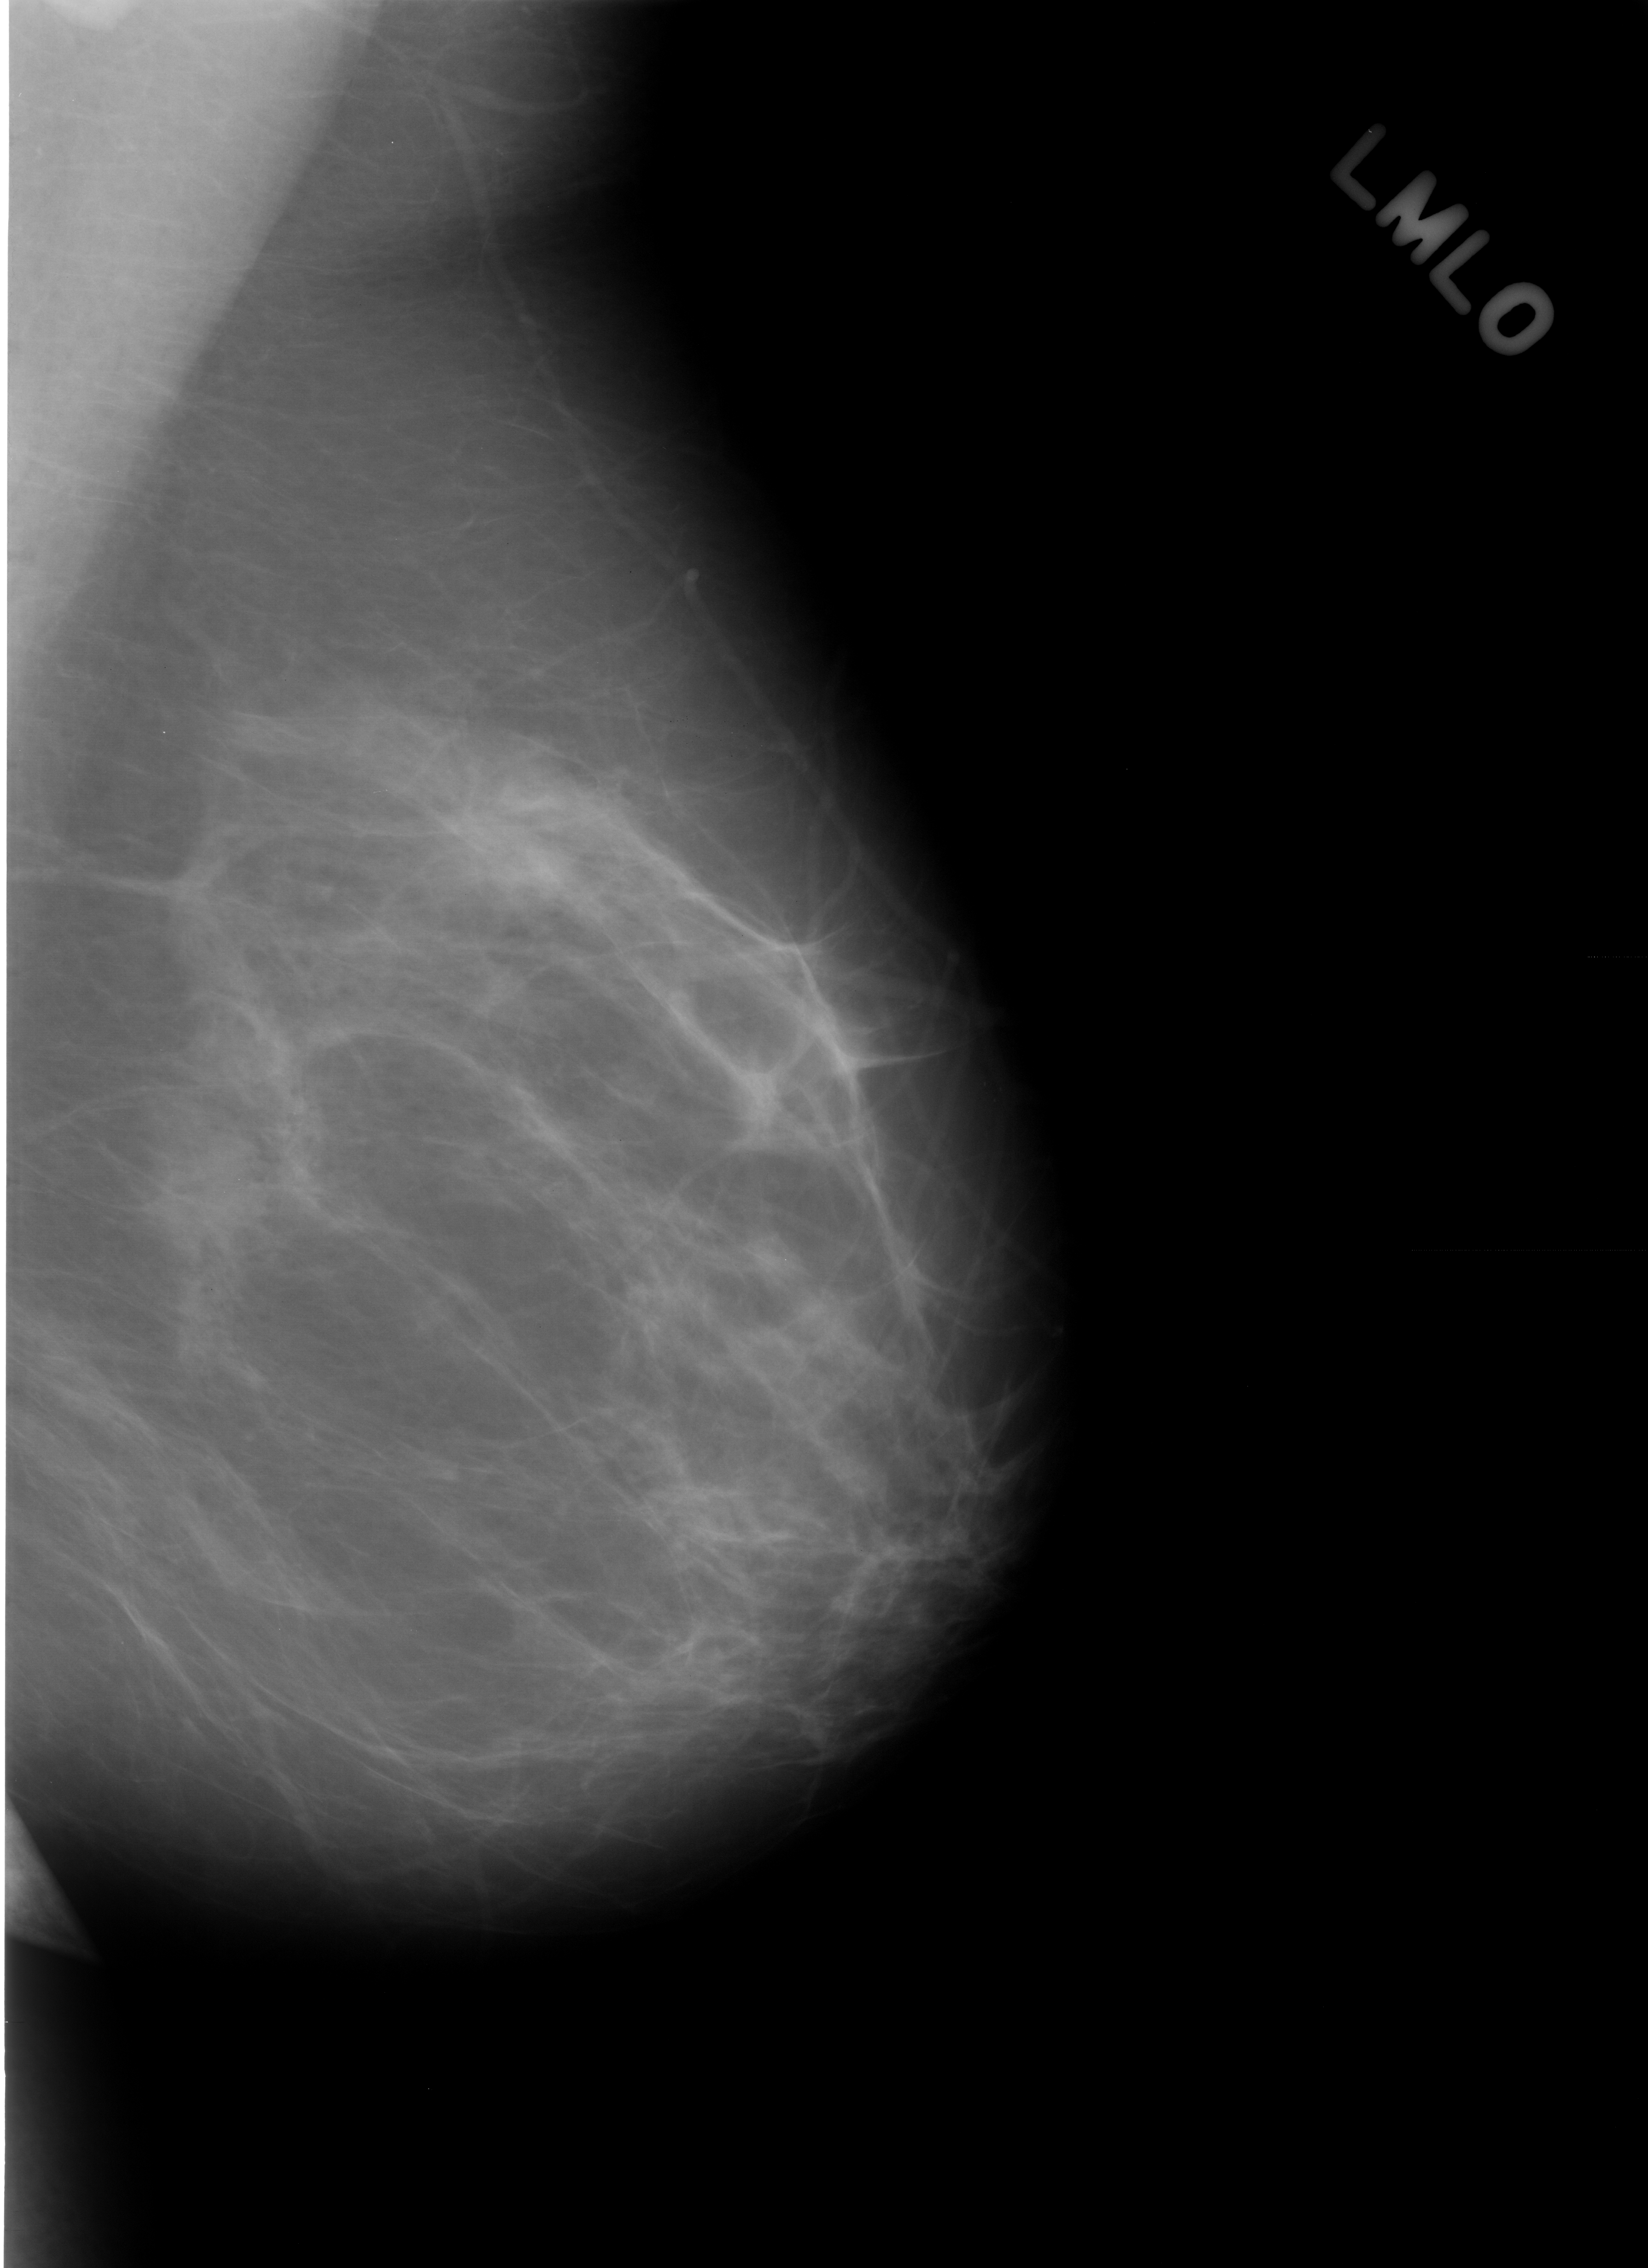
Scanned film-screen mammogram; left breast; mediolateral oblique (MLO) view.
Finding: mass, shape irregular, margins spiculated; BI-RADS assessment category 3; benign without callback (not worked up further).